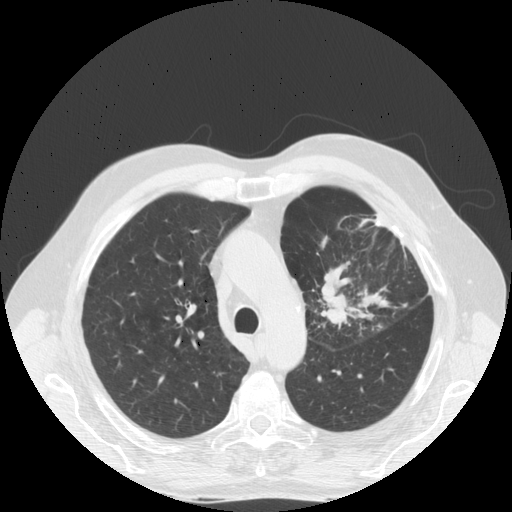
Low-dose screening chest CT, one axial slice; position 124 of 170 along the scan axis; reconstruction kernel STANDARD; 140 kVp; lung window (W 1500 / L -600 HU); 2.5 mm slice thickness; 512 × 512 image matrix, field of view 380 × 380 mm.
Structures marked on this image (outlined manually by an expert reader):
- lesion 1 (tumor, upper lobe of left lung): bounding box <320,282,351,327> (left, top, right, bottom; pixels)